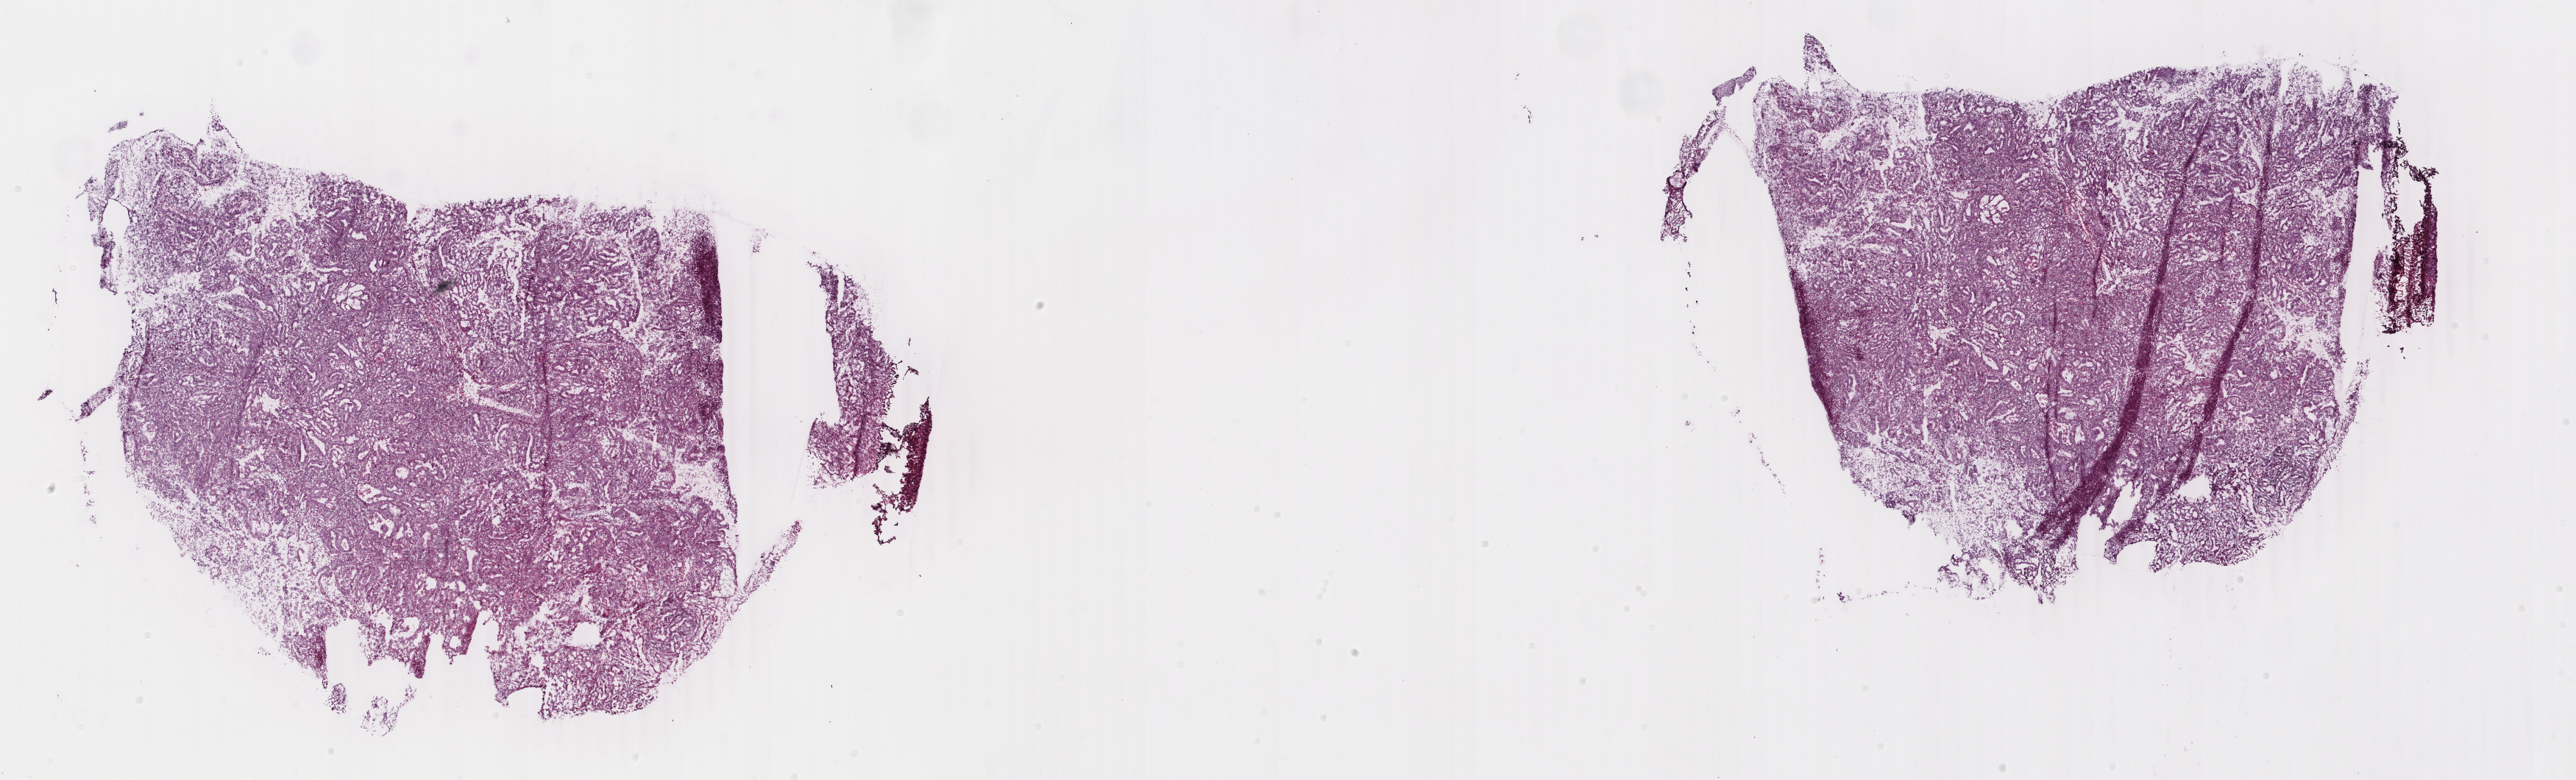
Whole-slide histology image, H&E-stained, whole scanned area (about 27.8 x 8.4 mm) shown as a low-resolution overview; frozen section from the bottom of the tissue portion; primary tumour sample from the uterus. Patient: female, age at initial diagnosis 60 years. Histologic grade: G1 (well differentiated). Pathologist review of this section (percent, as recorded): tumour cells 68%, tumour nuclei 70%, normal cells 15%, stromal cells 2%, necrosis 15%. Infiltration values recorded for this section: lymphocyte infiltration 24%, monocyte infiltration 1%, neutrophil infiltration 1%.
* FIGO stage: IIIA
* histologic diagnosis: Endometrioid adenocarcinoma, NOS (endometrium)